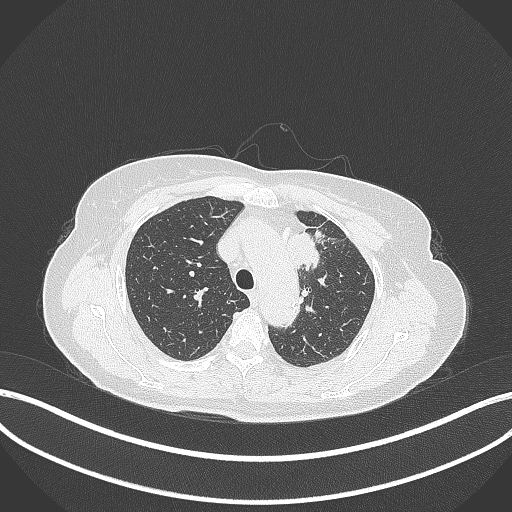
Chest CT, one axial slice. Position 251 of 369 along the scan axis. Reconstruction kernel B70f. 120 kVp. Lung window (W 1500 / L -600 HU). 512 × 512 image matrix. Patient: female, 65 years. From the clinical record (not read from this slice): clinical TNM (as recorded): T2a N0 M0.
Outlined on this slice (bounding box drawn by a radiologist):
- lung tumour (recorded histology: adenocarcinoma): bounding box (x1, y1, x2, y2) in pixels: (287, 229, 321, 273)